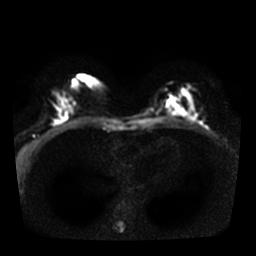
Breast MRI, one axial slice. Diffusion-weighted series; image 2 of 4 stored at this slice position (different b-values; order by instance number). 3 T. 5 mm slice thickness. 256 × 256 image matrix, field of view 320 × 320 mm. Female patient.
Structures marked on this image (outlined manually by an expert reader):
- tumour on diffusion-weighted imaging: box from (x=172, y=102) to (x=186, y=115) px